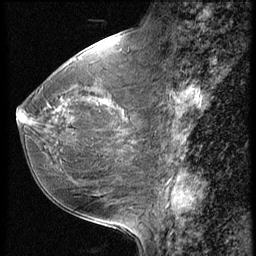
Breast MRI (dynamic contrast-enhanced), one sagittal slice. Position 23 of 56 along the scan axis. 3 images stored at this slice position (order not interpretable as contrast timing). 1.5 T. TE 4.2 ms, TR 9 ms. 256 × 256 image matrix, field of view 180 × 180 mm. Patient: female, 49 years. From the clinical record (not read from this slice): setting: breast cancer imaged before/during neoadjuvant chemotherapy; receptor status: HER2-positive.
Structures marked on this image (semi-automatically segmented with operator editing):
- analysis volume of interest (the breast-tissue region the enhancement analysis was run in; not a lesion): bounding box <17,74,148,198> (left, top, right, bottom; pixels)
- tumour enhancement mask (voxels above the 140 % enhancement threshold inside the analysis volume of interest): <18,108,61,125>